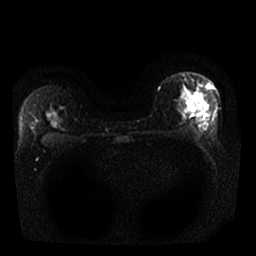
Breast MRI, one axial slice. Diffusion-weighted series; image 2 of 4 stored at this slice position (different b-values; order by instance number). 1.5 T. 256 × 256 image matrix, field of view 320 × 320 mm. Female patient.
Structures marked on this image (expert manual segmentation):
- tumour on diffusion-weighted imaging: bounding box [x1, y1, x2, y2] px = [187, 93, 198, 108]